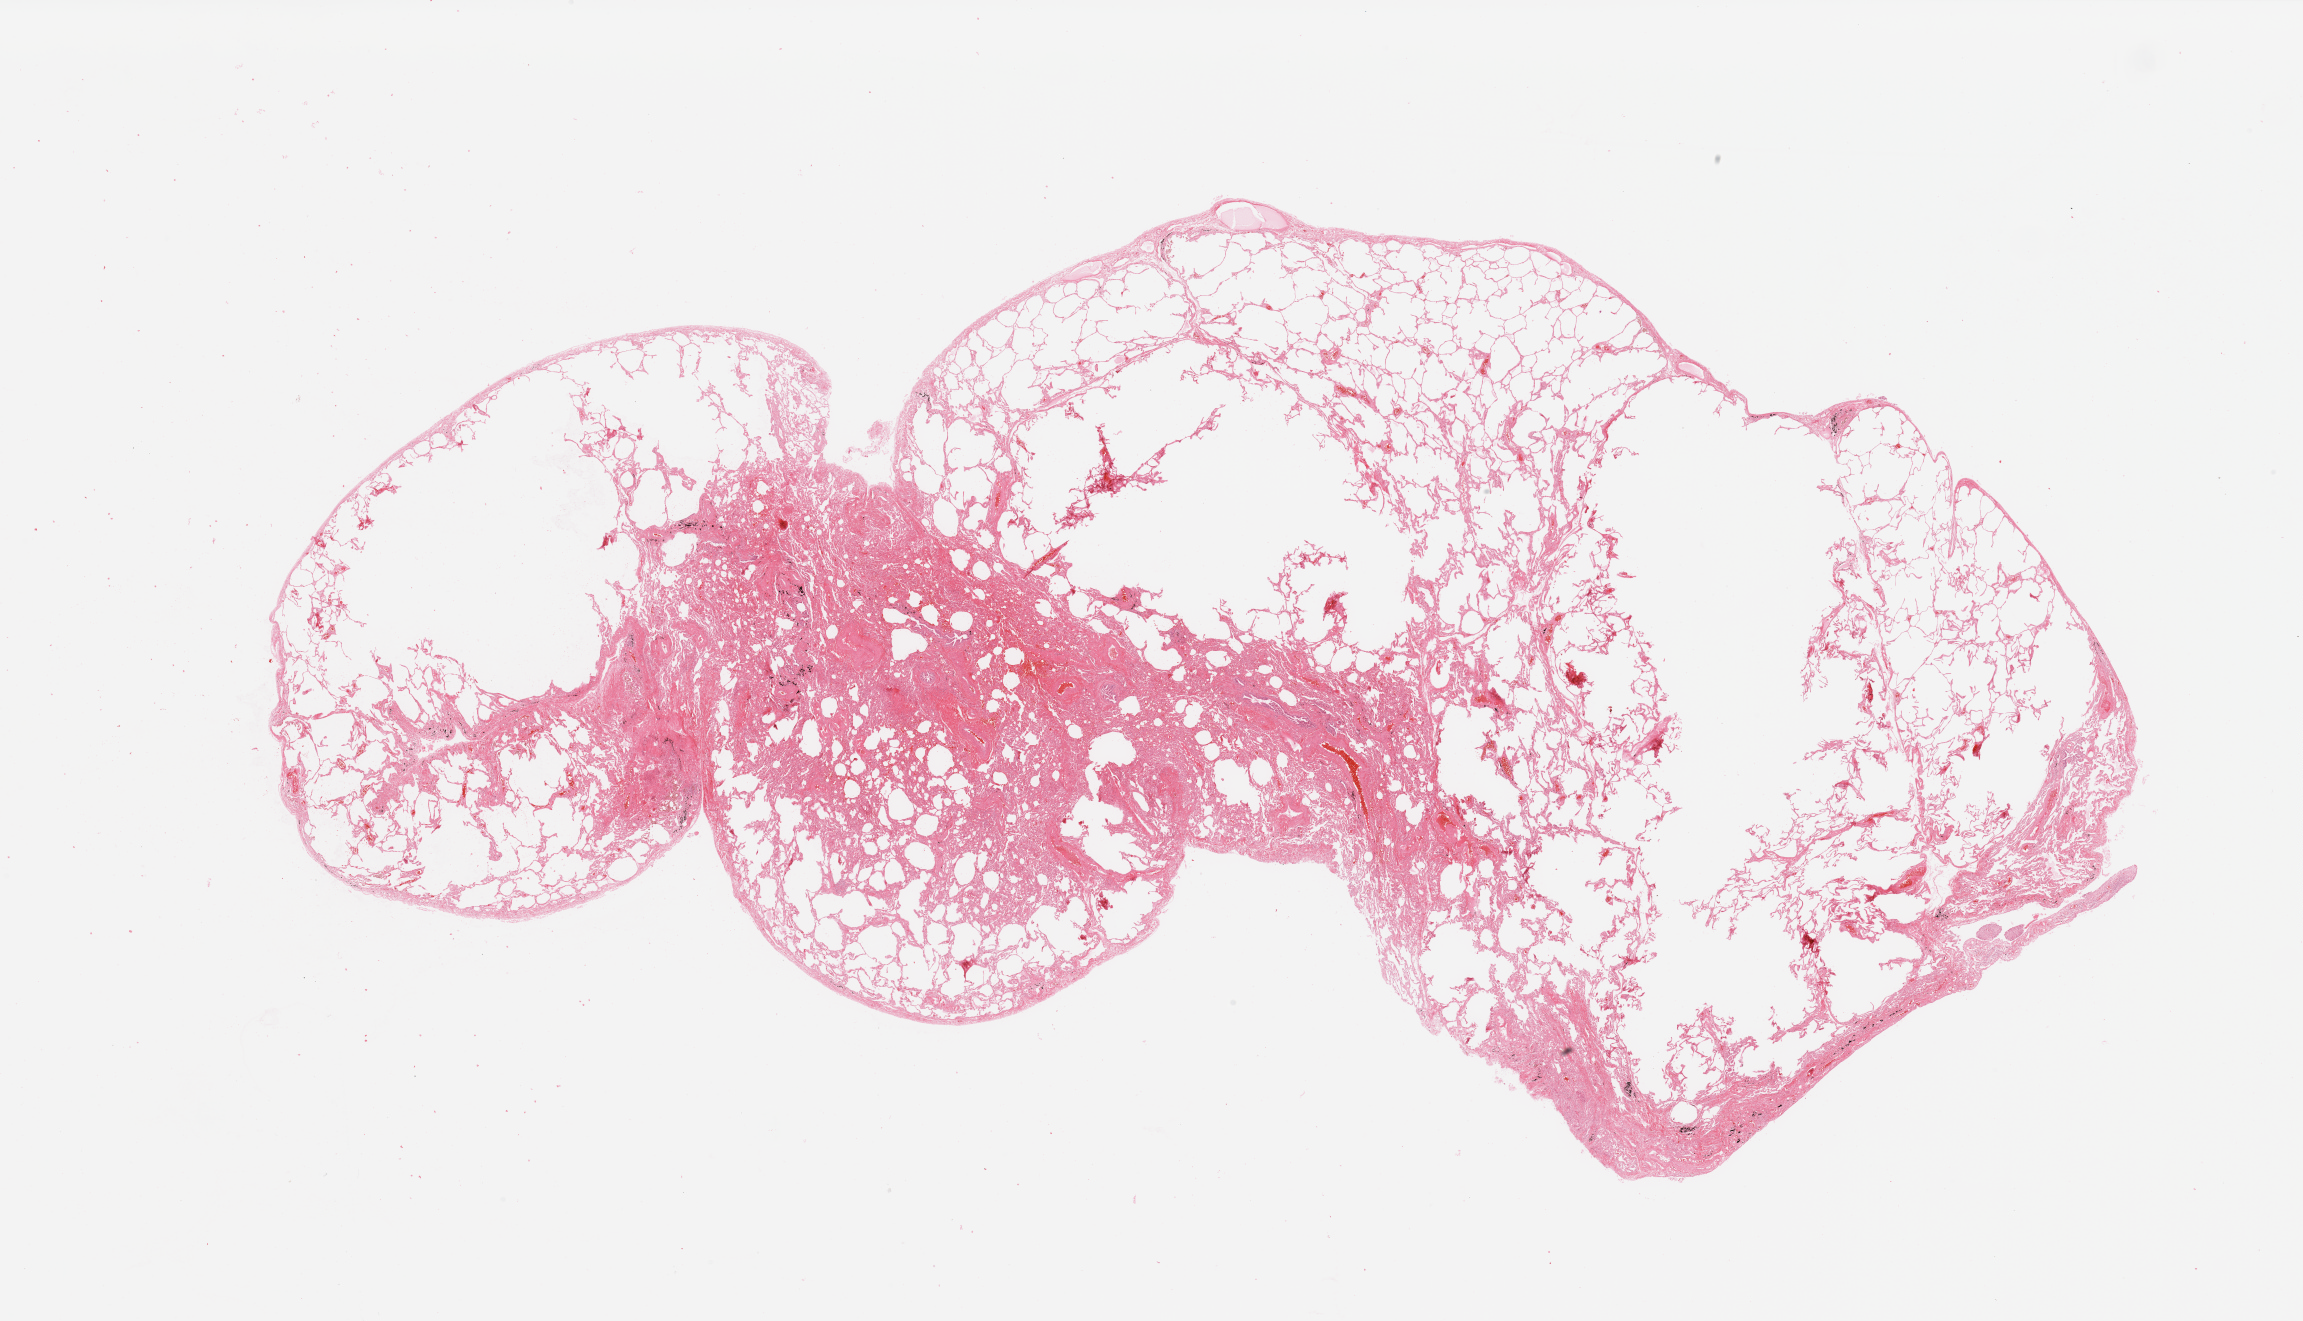
Hematoxylin and eosin (H&E) stained whole-slide image — low-resolution overview of the scanned area, about 36.4 x 20.9 mm. Normal (non-tumour) tissue sample, sampled site: lung. Patient: male, age 59 years.
This section: normal (non-tumour) tissue from the same patient. Patient diagnosis: Adenocarcinoma, NOS.